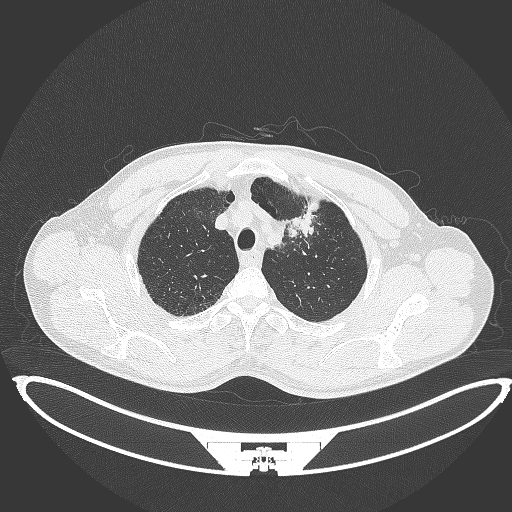
Chest CT, one axial slice. Slice 367 of 395 in the series (ordered by position). Lung window (W 1500 / L -600 HU). 1 mm slice thickness. 512 × 512 image matrix. Male patient, age 60 years. From the clinical record (not read from this slice): clinical TNM (as recorded): T2a N0 M0; histopathological grade: G1-G2.
Structures marked on this image (rectangle marked by the reading radiologist):
- lung tumour (recorded histology: squamous cell carcinoma): bounding box <287,207,317,242> (left, top, right, bottom; pixels)